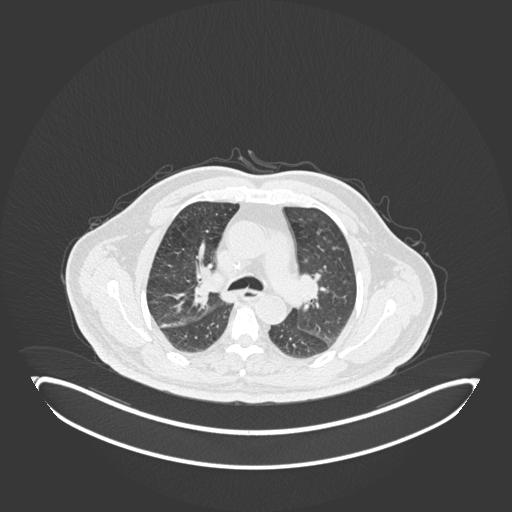
Chest CT, one axial slice. Slice 119 of 247 in the series (ordered by position). Reconstruction kernel B30f. Lung window (W 1500 / L -600 HU). 512 × 512 image matrix, field of view 500 × 500 mm. Patient: male, 72 years. From the clinical record (not read from this slice): clinical TNM (as recorded): T1c N0 M0; histopathological grade: G2.
Outlined on this slice (bounding box drawn by a radiologist):
- lung tumour (recorded histology: squamous cell carcinoma): bounding box <188,264,212,308> (left, top, right, bottom; pixels)